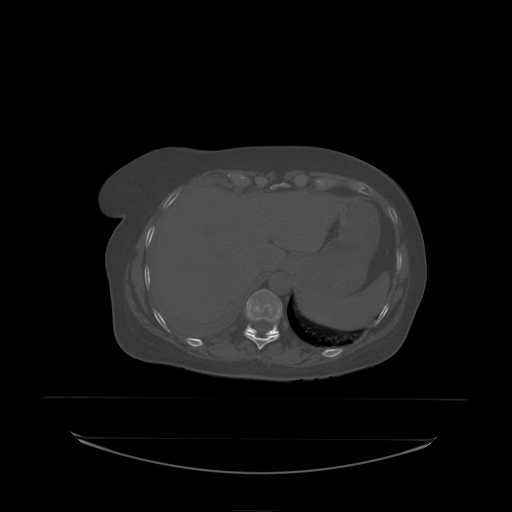
CT including the spine, one axial slice. Position 110 of 242 along the scan axis. Bone window (W 1800 / L 400 HU). 2.5 mm slice thickness. 512 × 512 image matrix, field of view 500 × 500 mm. Patient: female, 53 years. Case-level facts recorded for this patient, not image findings: primary cancer: lung; vertebrae with lytic lesions (as recorded): T7, L1.
Annotated regions visible in this slice (semi-automatic segmentation, software-assisted and operator-edited):
- T10 vertebra: bounding box <244,332,279,338> (left, top, right, bottom; pixels)
- T11 vertebra: <246,290,283,336>